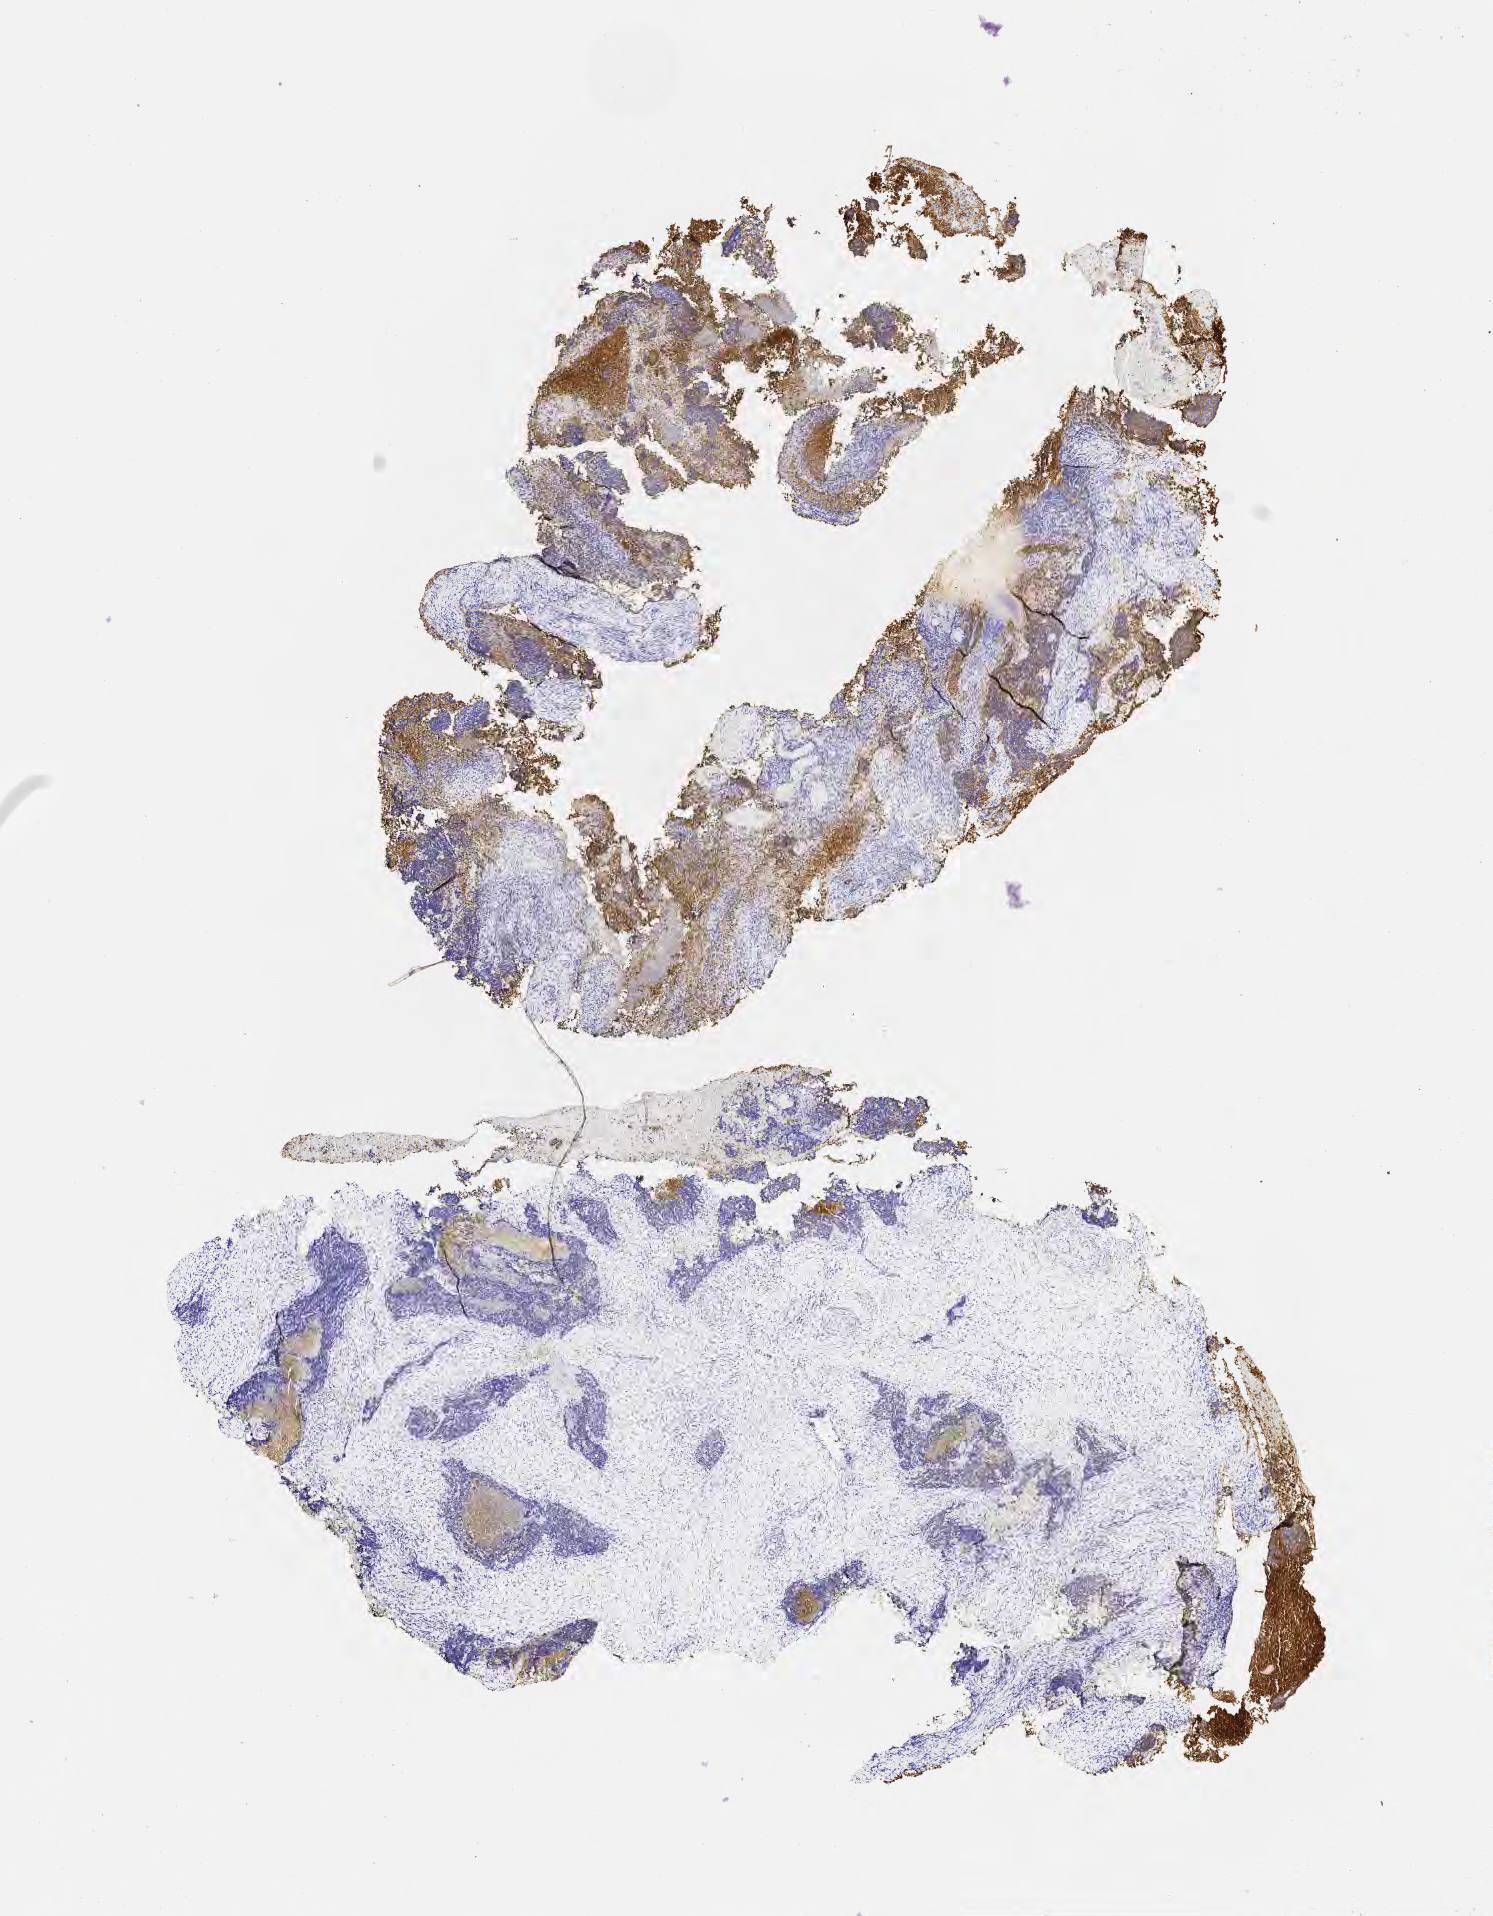
Immunohistochemistry (IHC) whole-slide image stained for MOC-31 (anti-EpCAM), whole scanned area (about 6.0 x 7.7 mm) shown as a low-resolution overview; tumor tissue; anatomic site: cervix. Patient: female, age 47 years.
Diagnosis: Squamous cell carcinoma, large cell, nonkeratinizing, NOS.